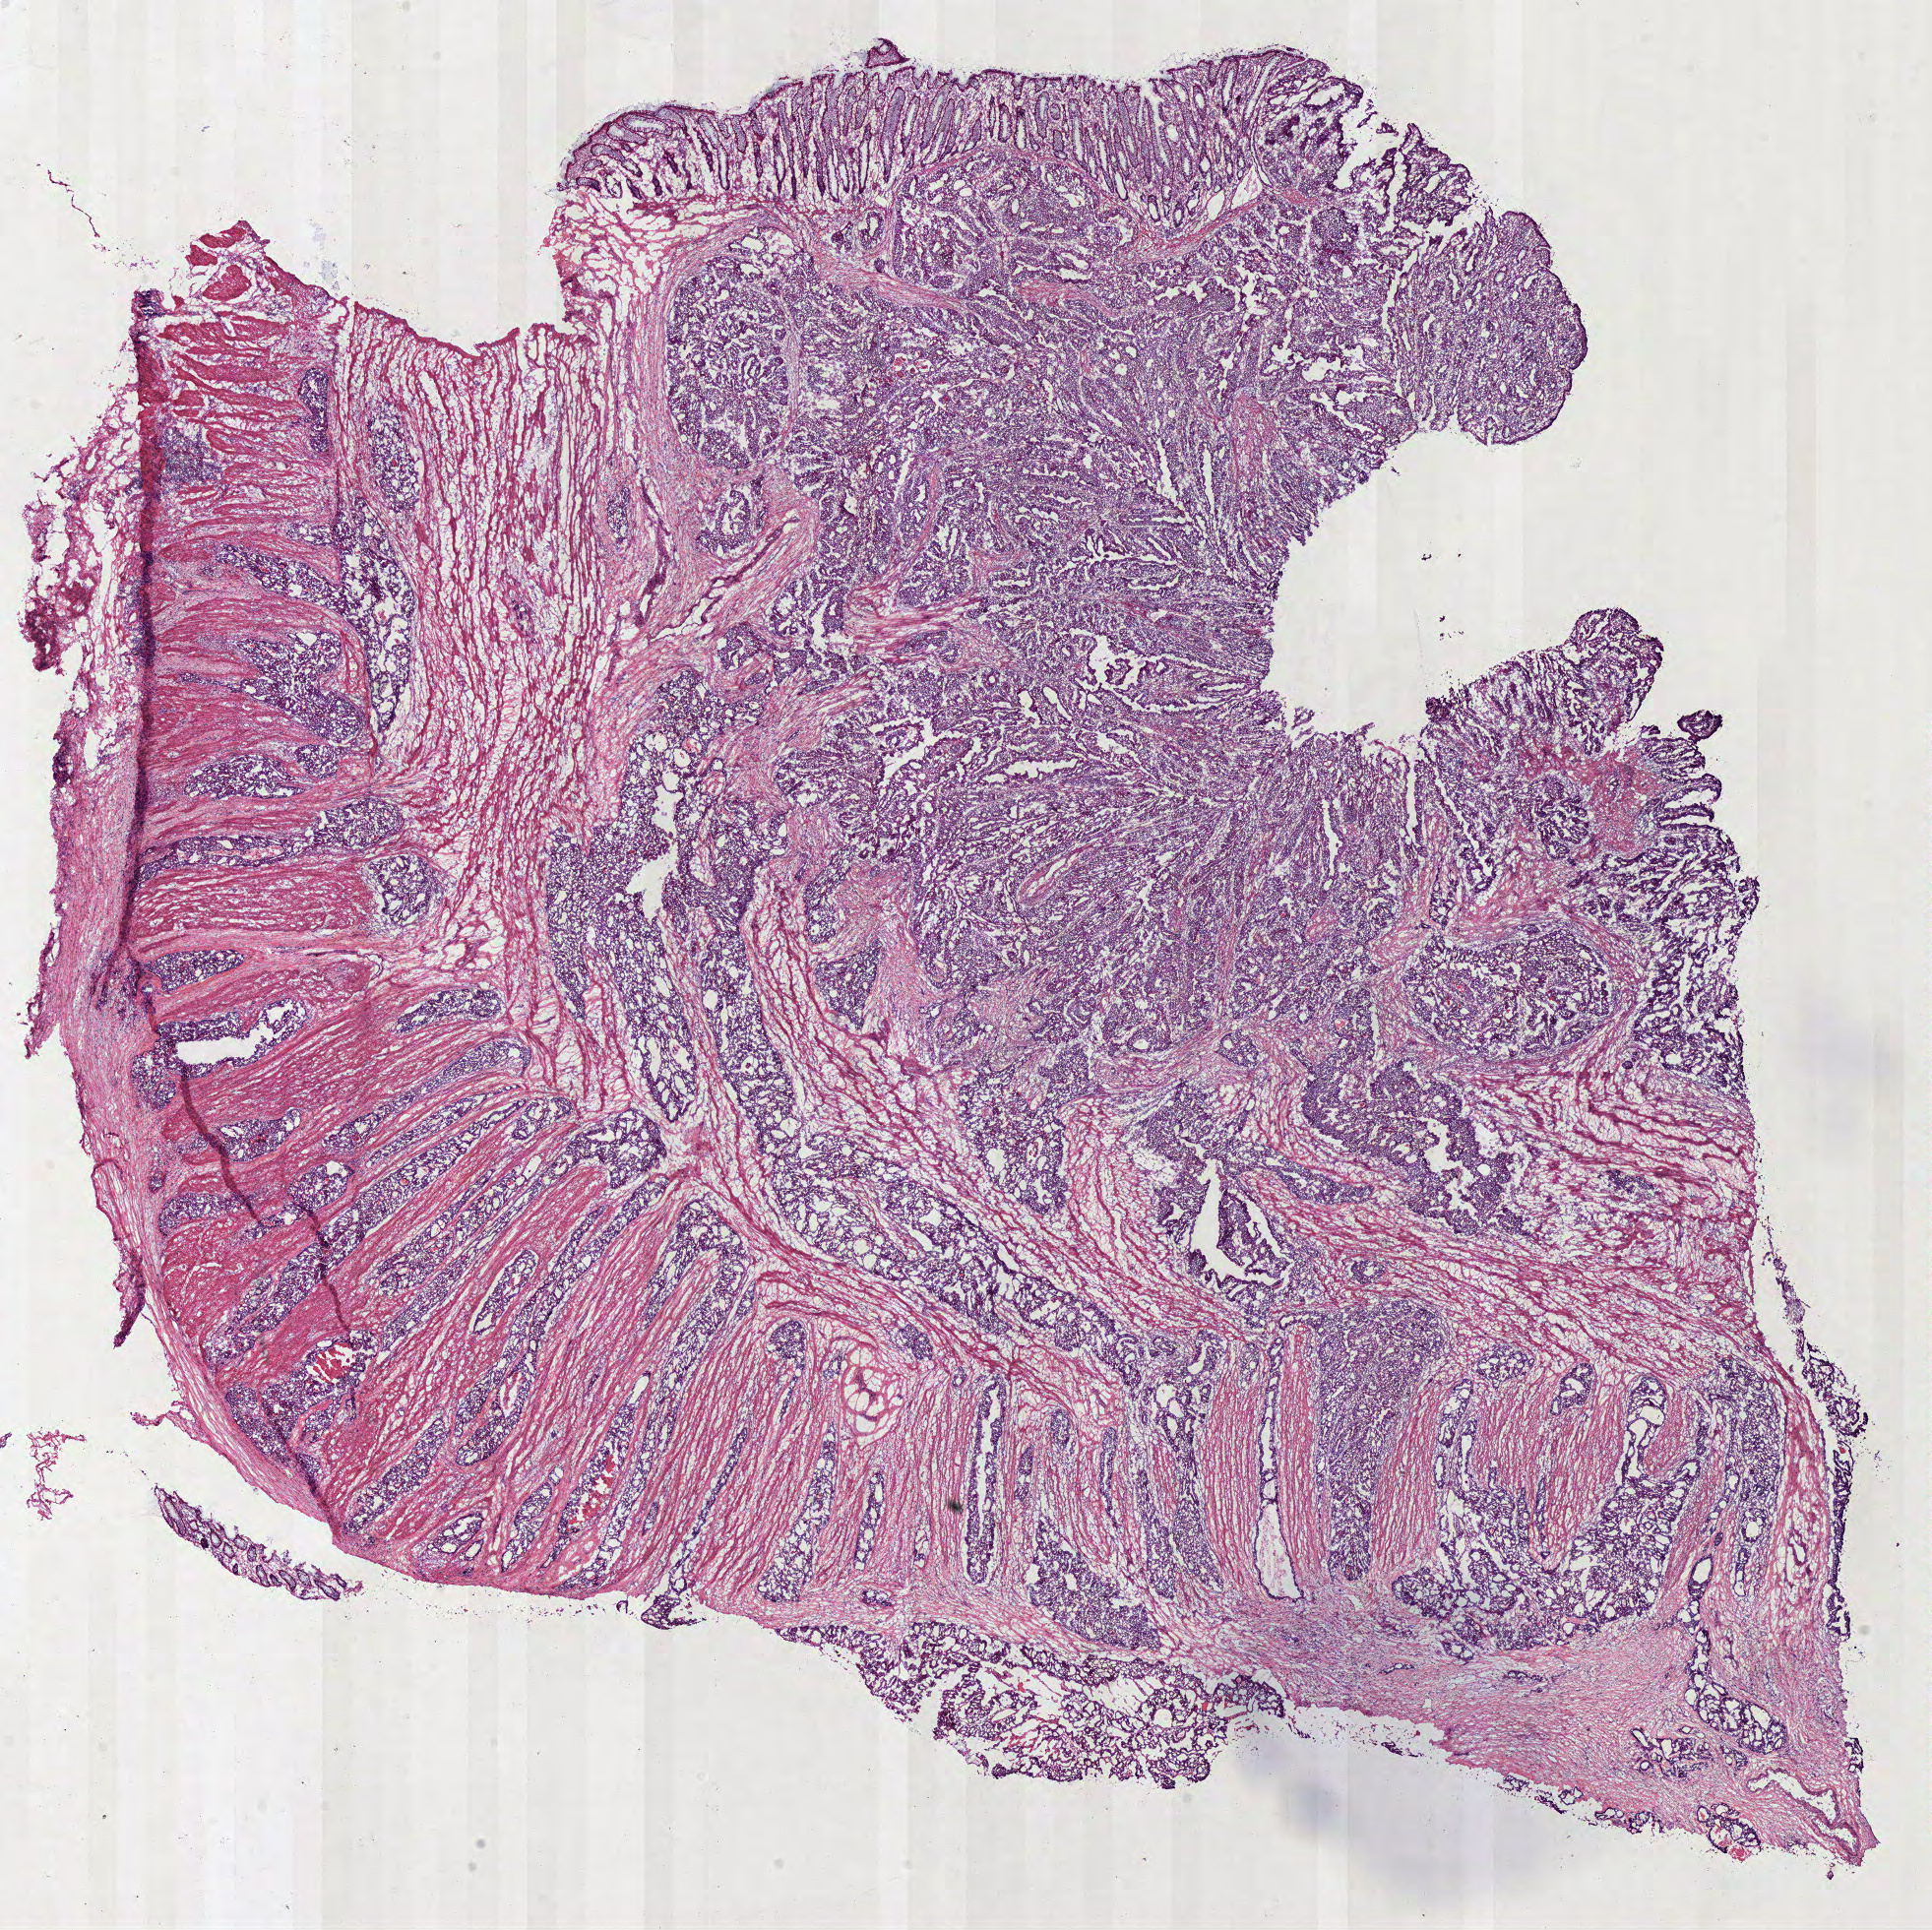
H&E-stained whole-slide image, a low-resolution overview of the entire scanned area, about 15.5 x 15.5 mm (from a 40x scan); frozen section from the bottom of the tissue portion; sample: primary tumour, rectum. Patient: female, age at initial diagnosis 71 years. Pathologist review of this section (percent, as recorded): tumour cells 81%, tumour nuclei 80%.
Histologic diagnosis: Adenocarcinoma, NOS.